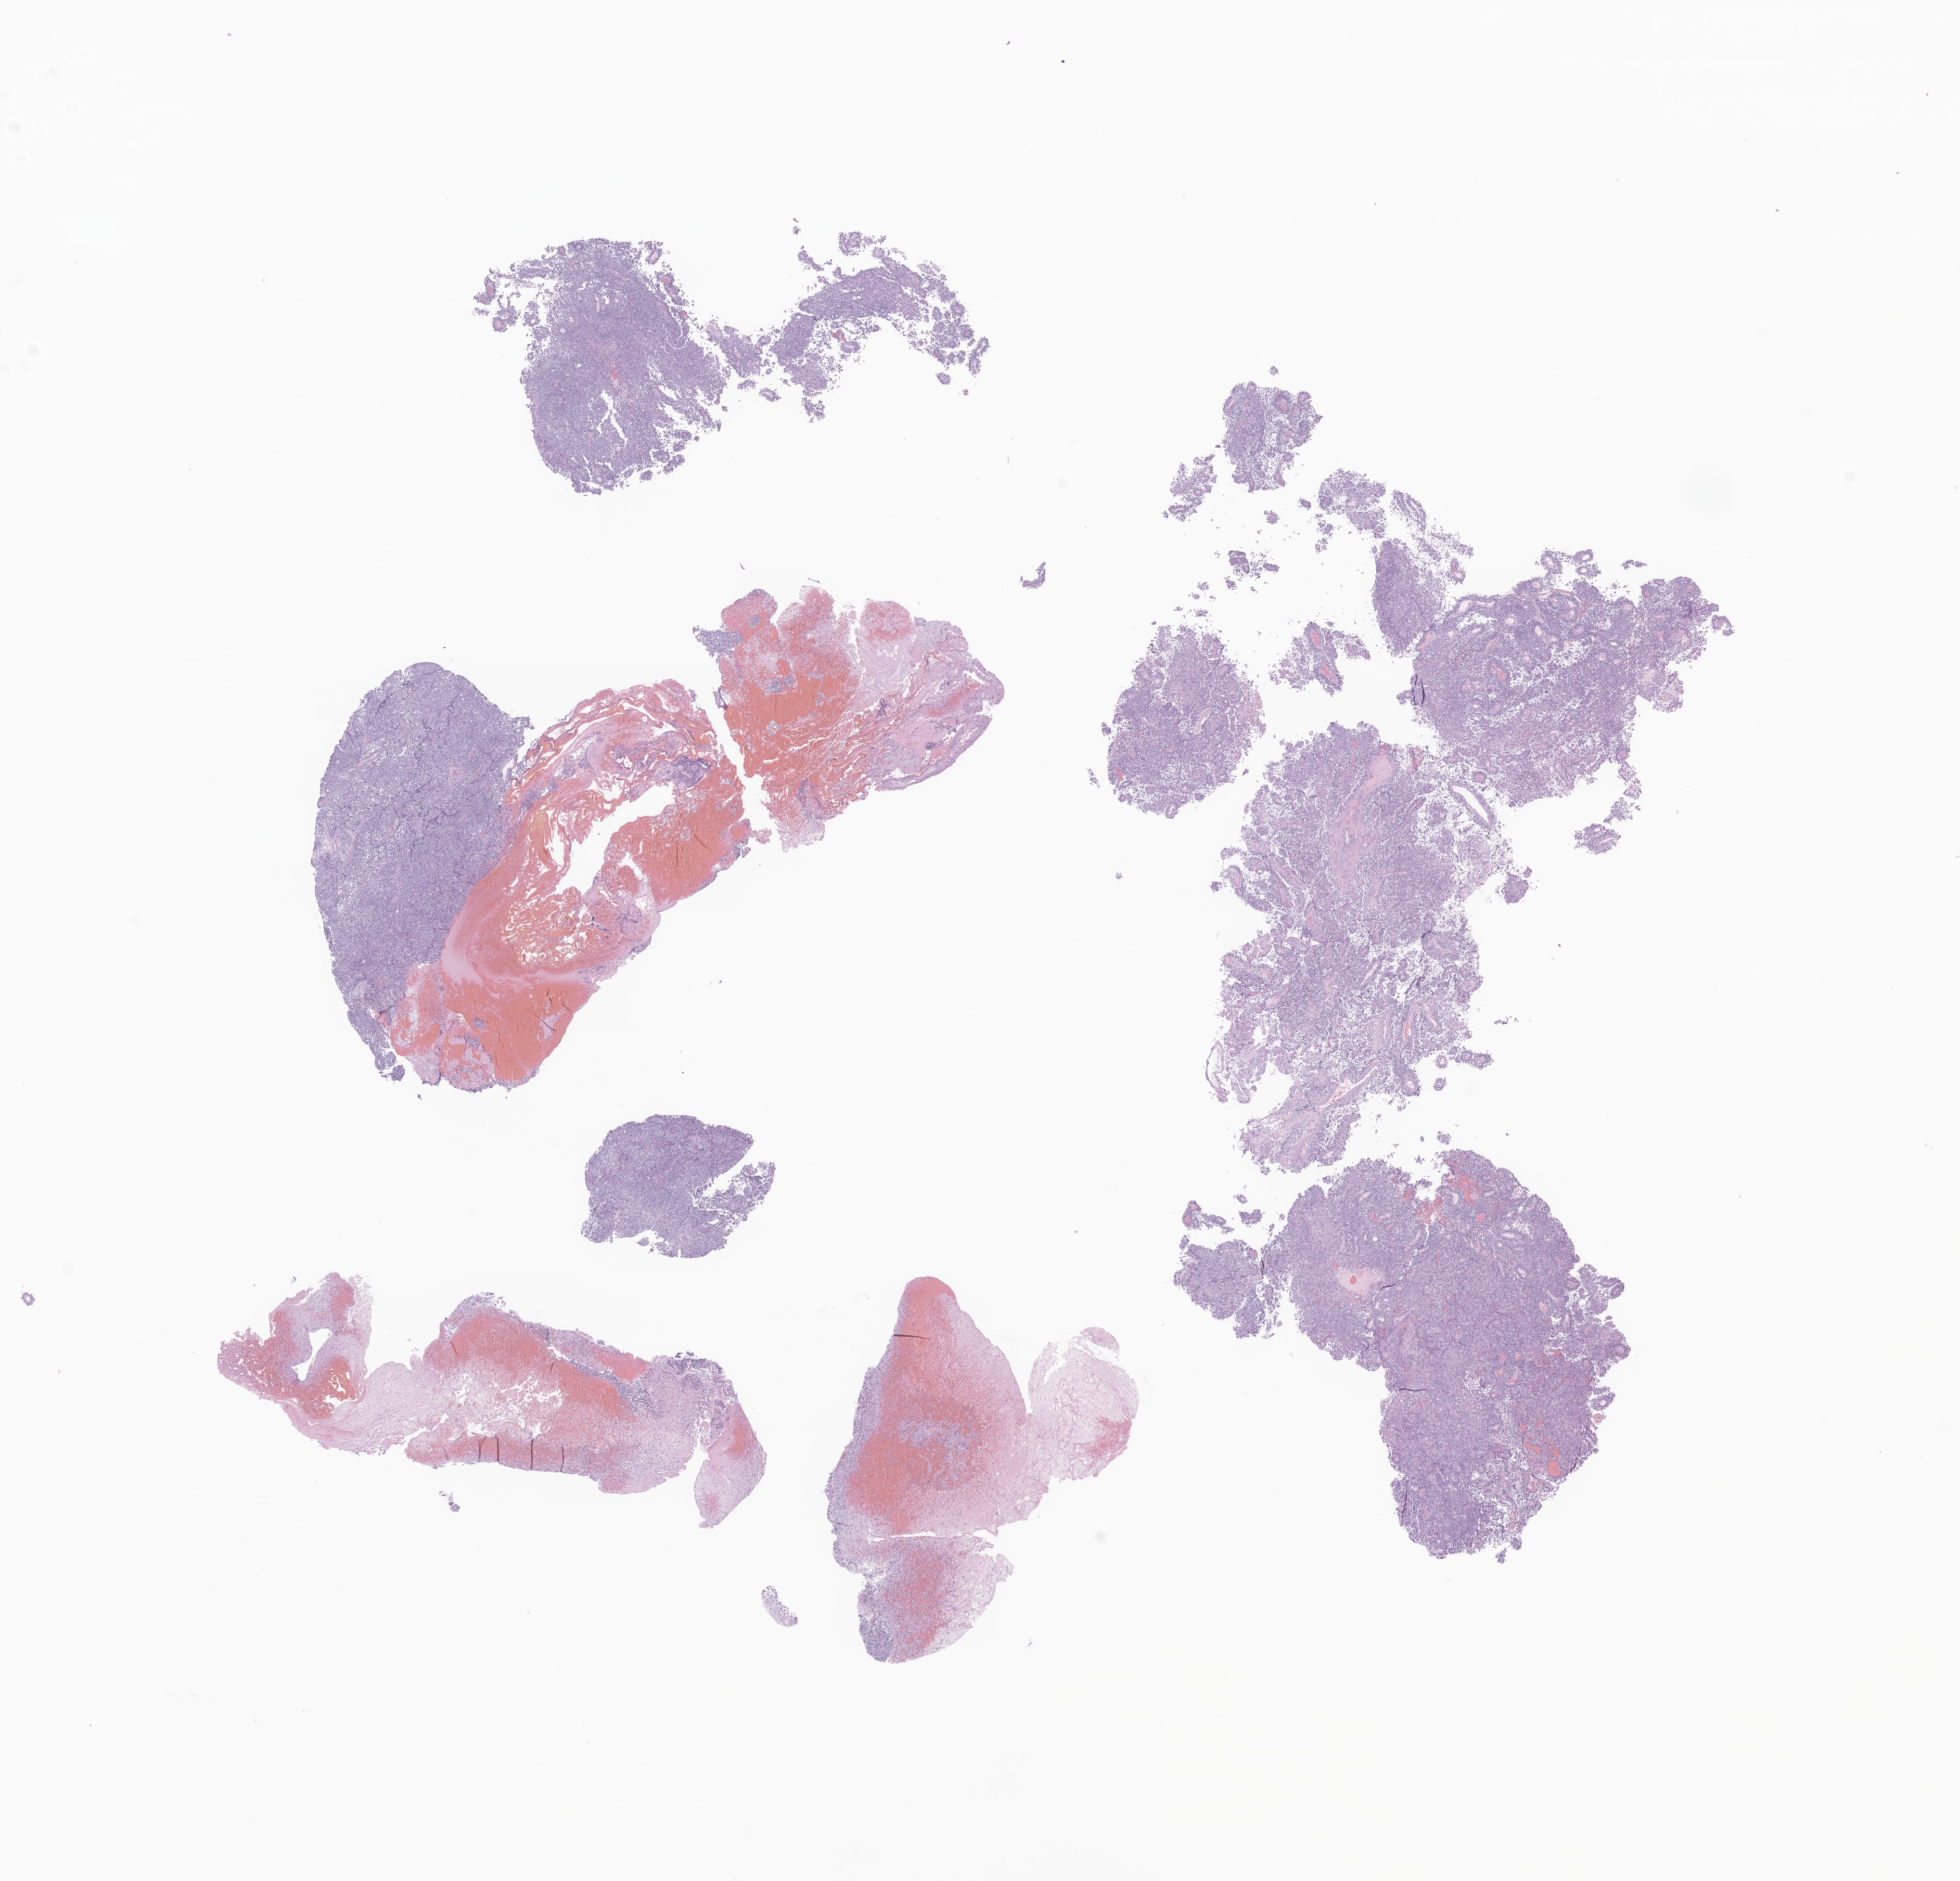
Hematoxylin and eosin (H&E) whole-slide image of tumor tissue from the brain — a low-resolution overview of the entire scanned area, about 17.2 x 16.5 mm, FFPE section. Patient: female, age 898 days (about 2.5 years).
- recorded diagnosis: Atypical teratoid/rhabdoid tumor